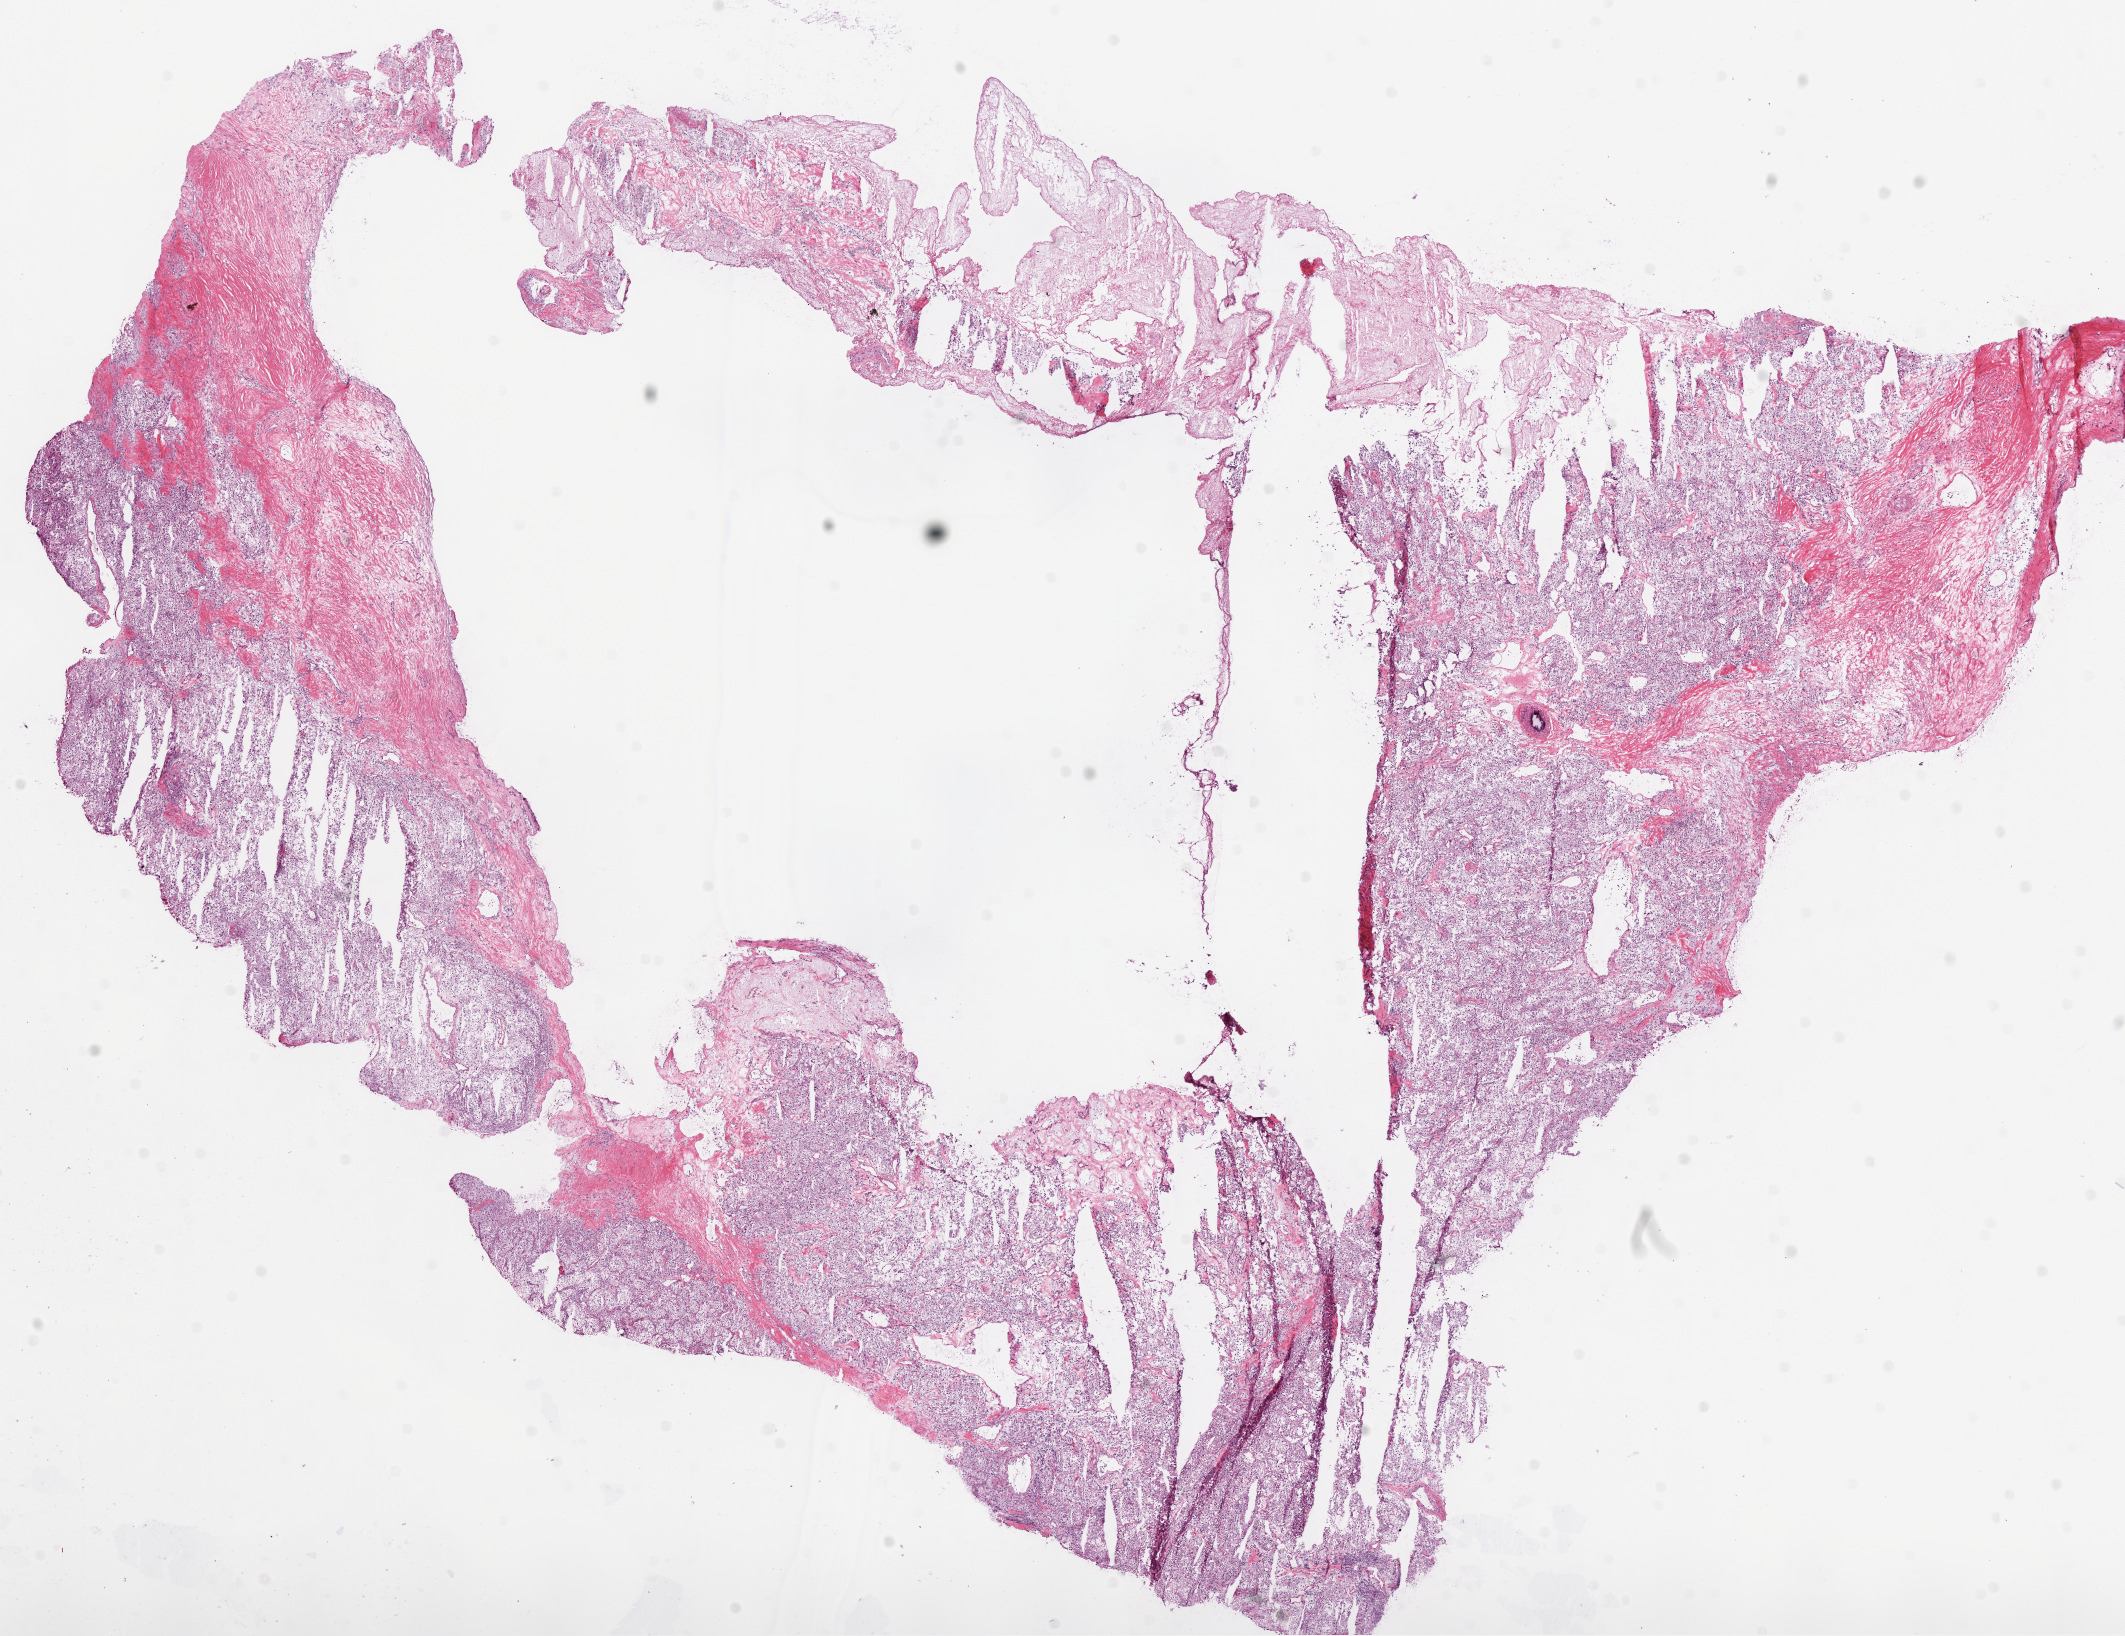
Whole-slide histology image, Hematoxylin and eosin (H&E) stained, low-resolution overview of the scanned area, about 17.1 x 13.1 mm. Frozen section. Primary tumour sample from the kidney. Patient: male, age at initial diagnosis 64 years.
Diagnosis: Clear cell adenocarcinoma, NOS.